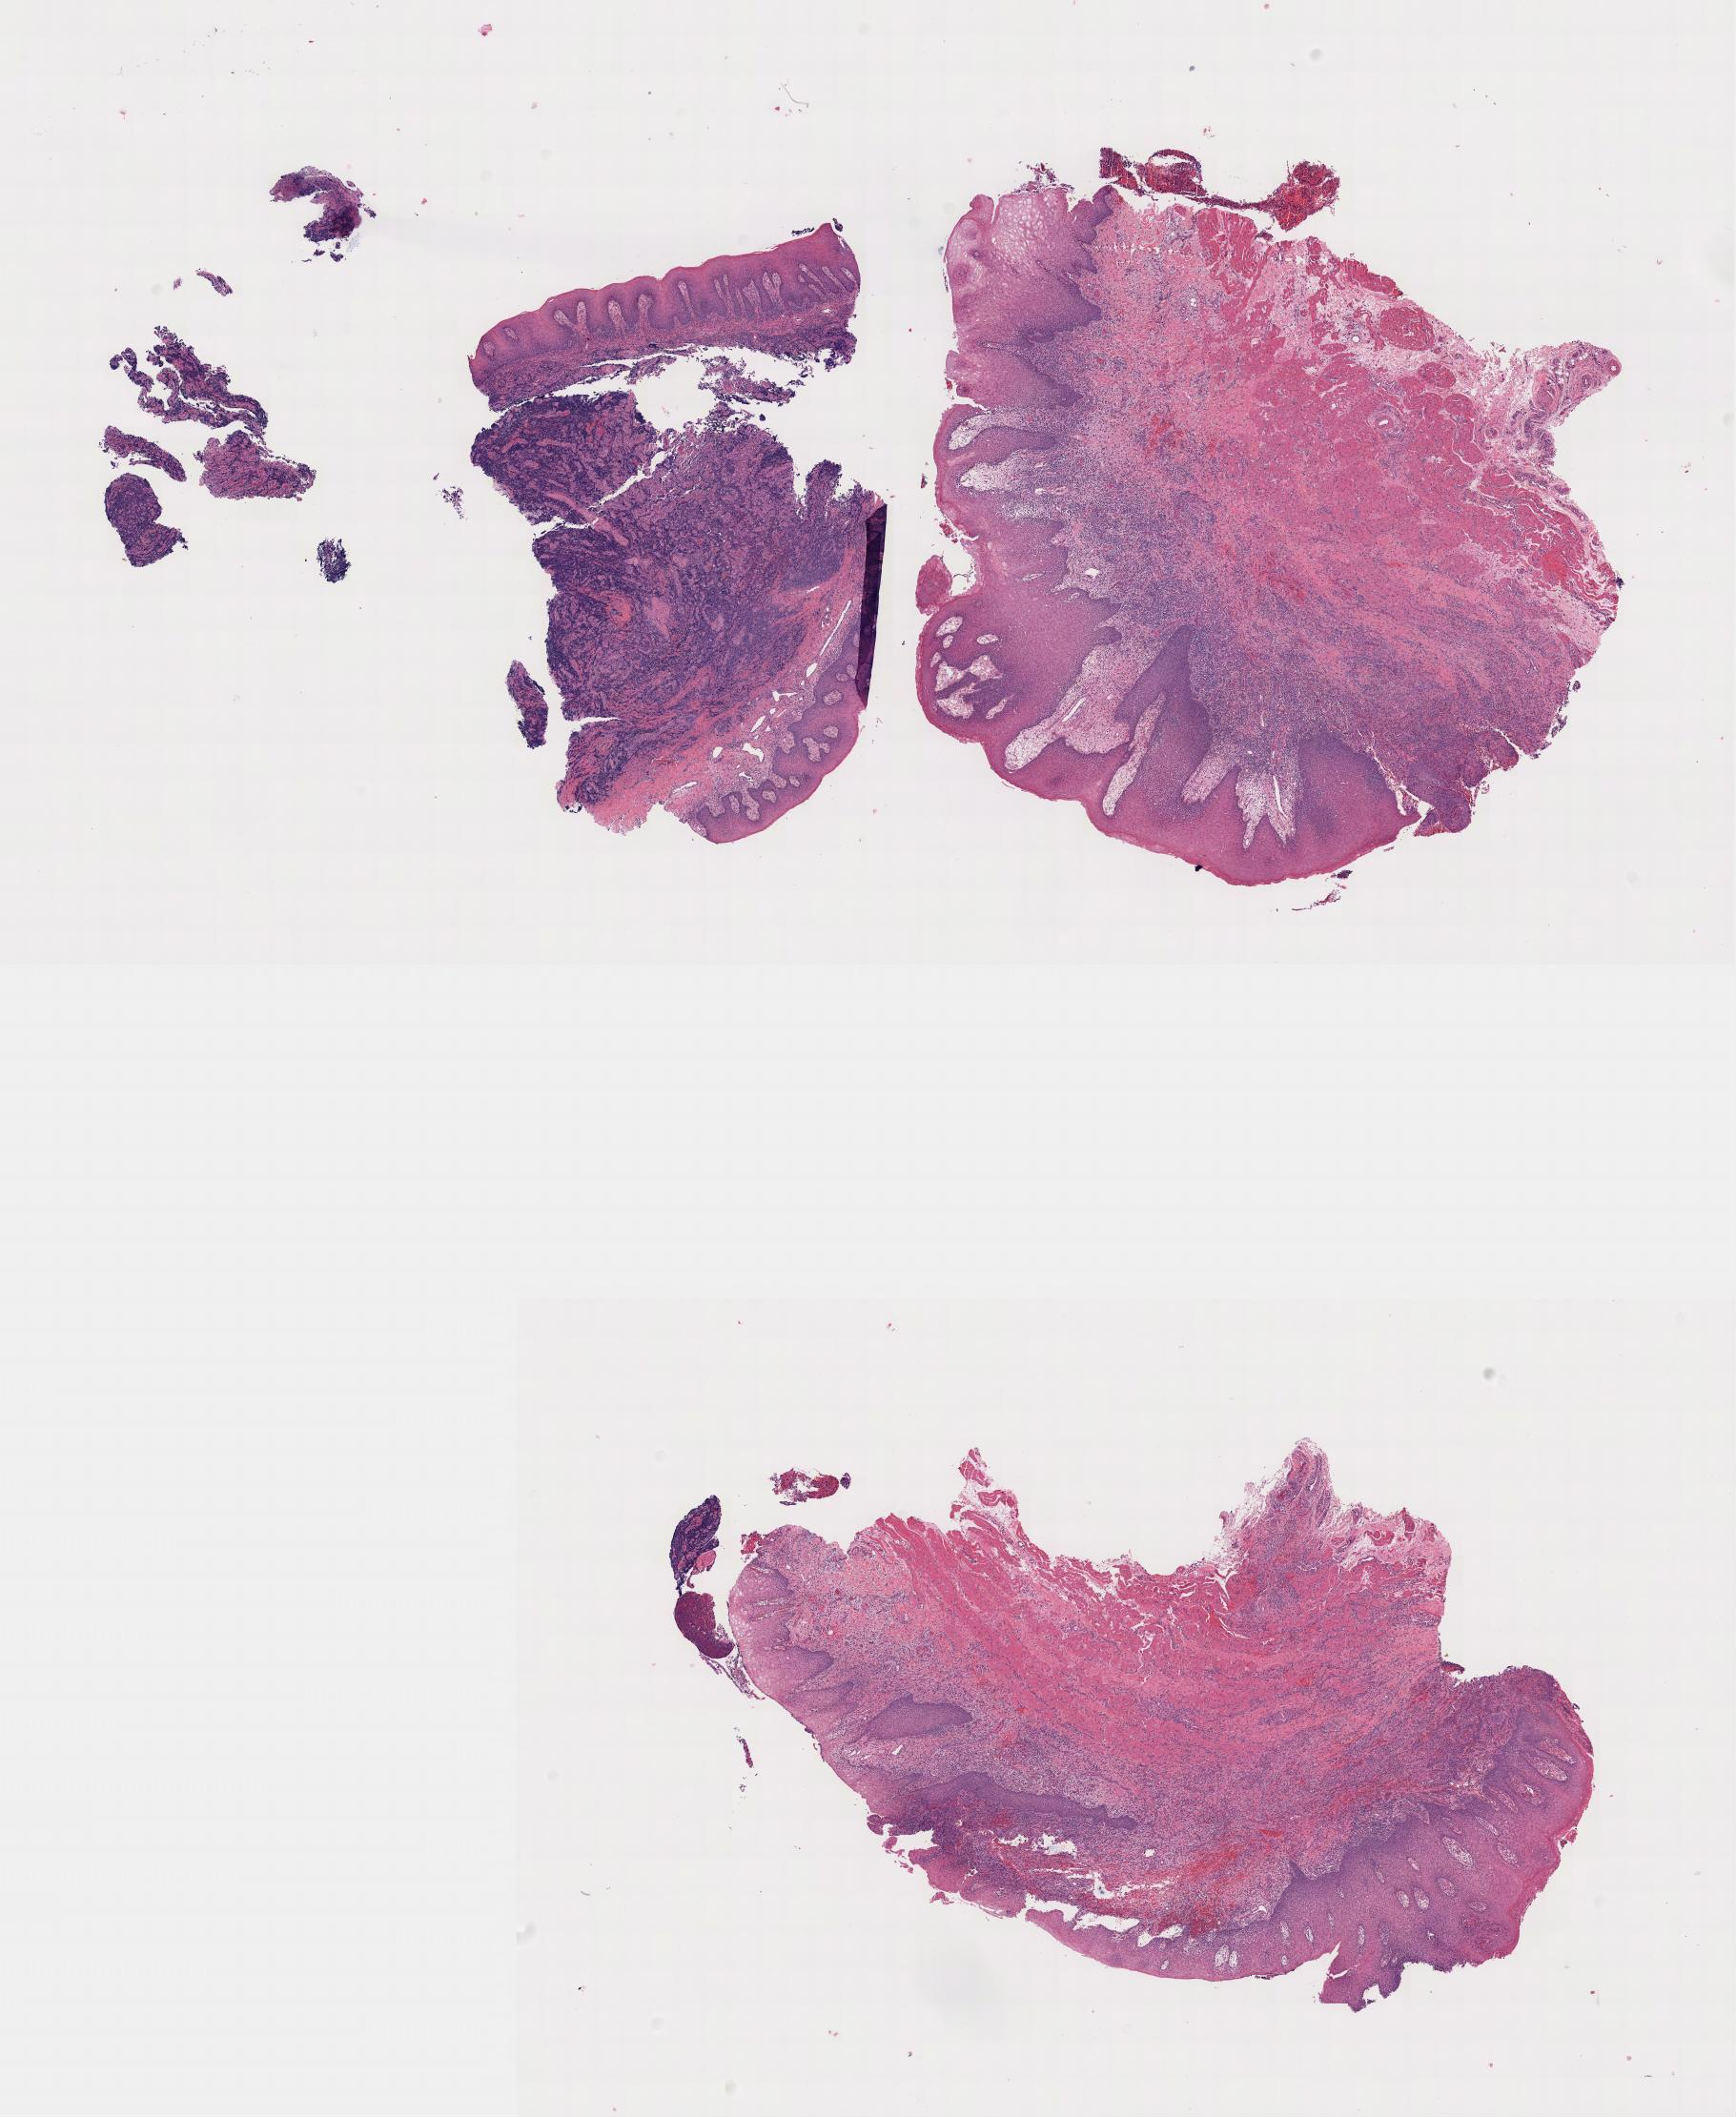
Haematoxylin and eosin whole-slide image — a low-resolution overview of the entire scanned area, tumor tissue, anatomic site: mandible. Patient: male, age at initial diagnosis 5 years.
Histologic diagnosis: Burkitt lymphoma, NOS.